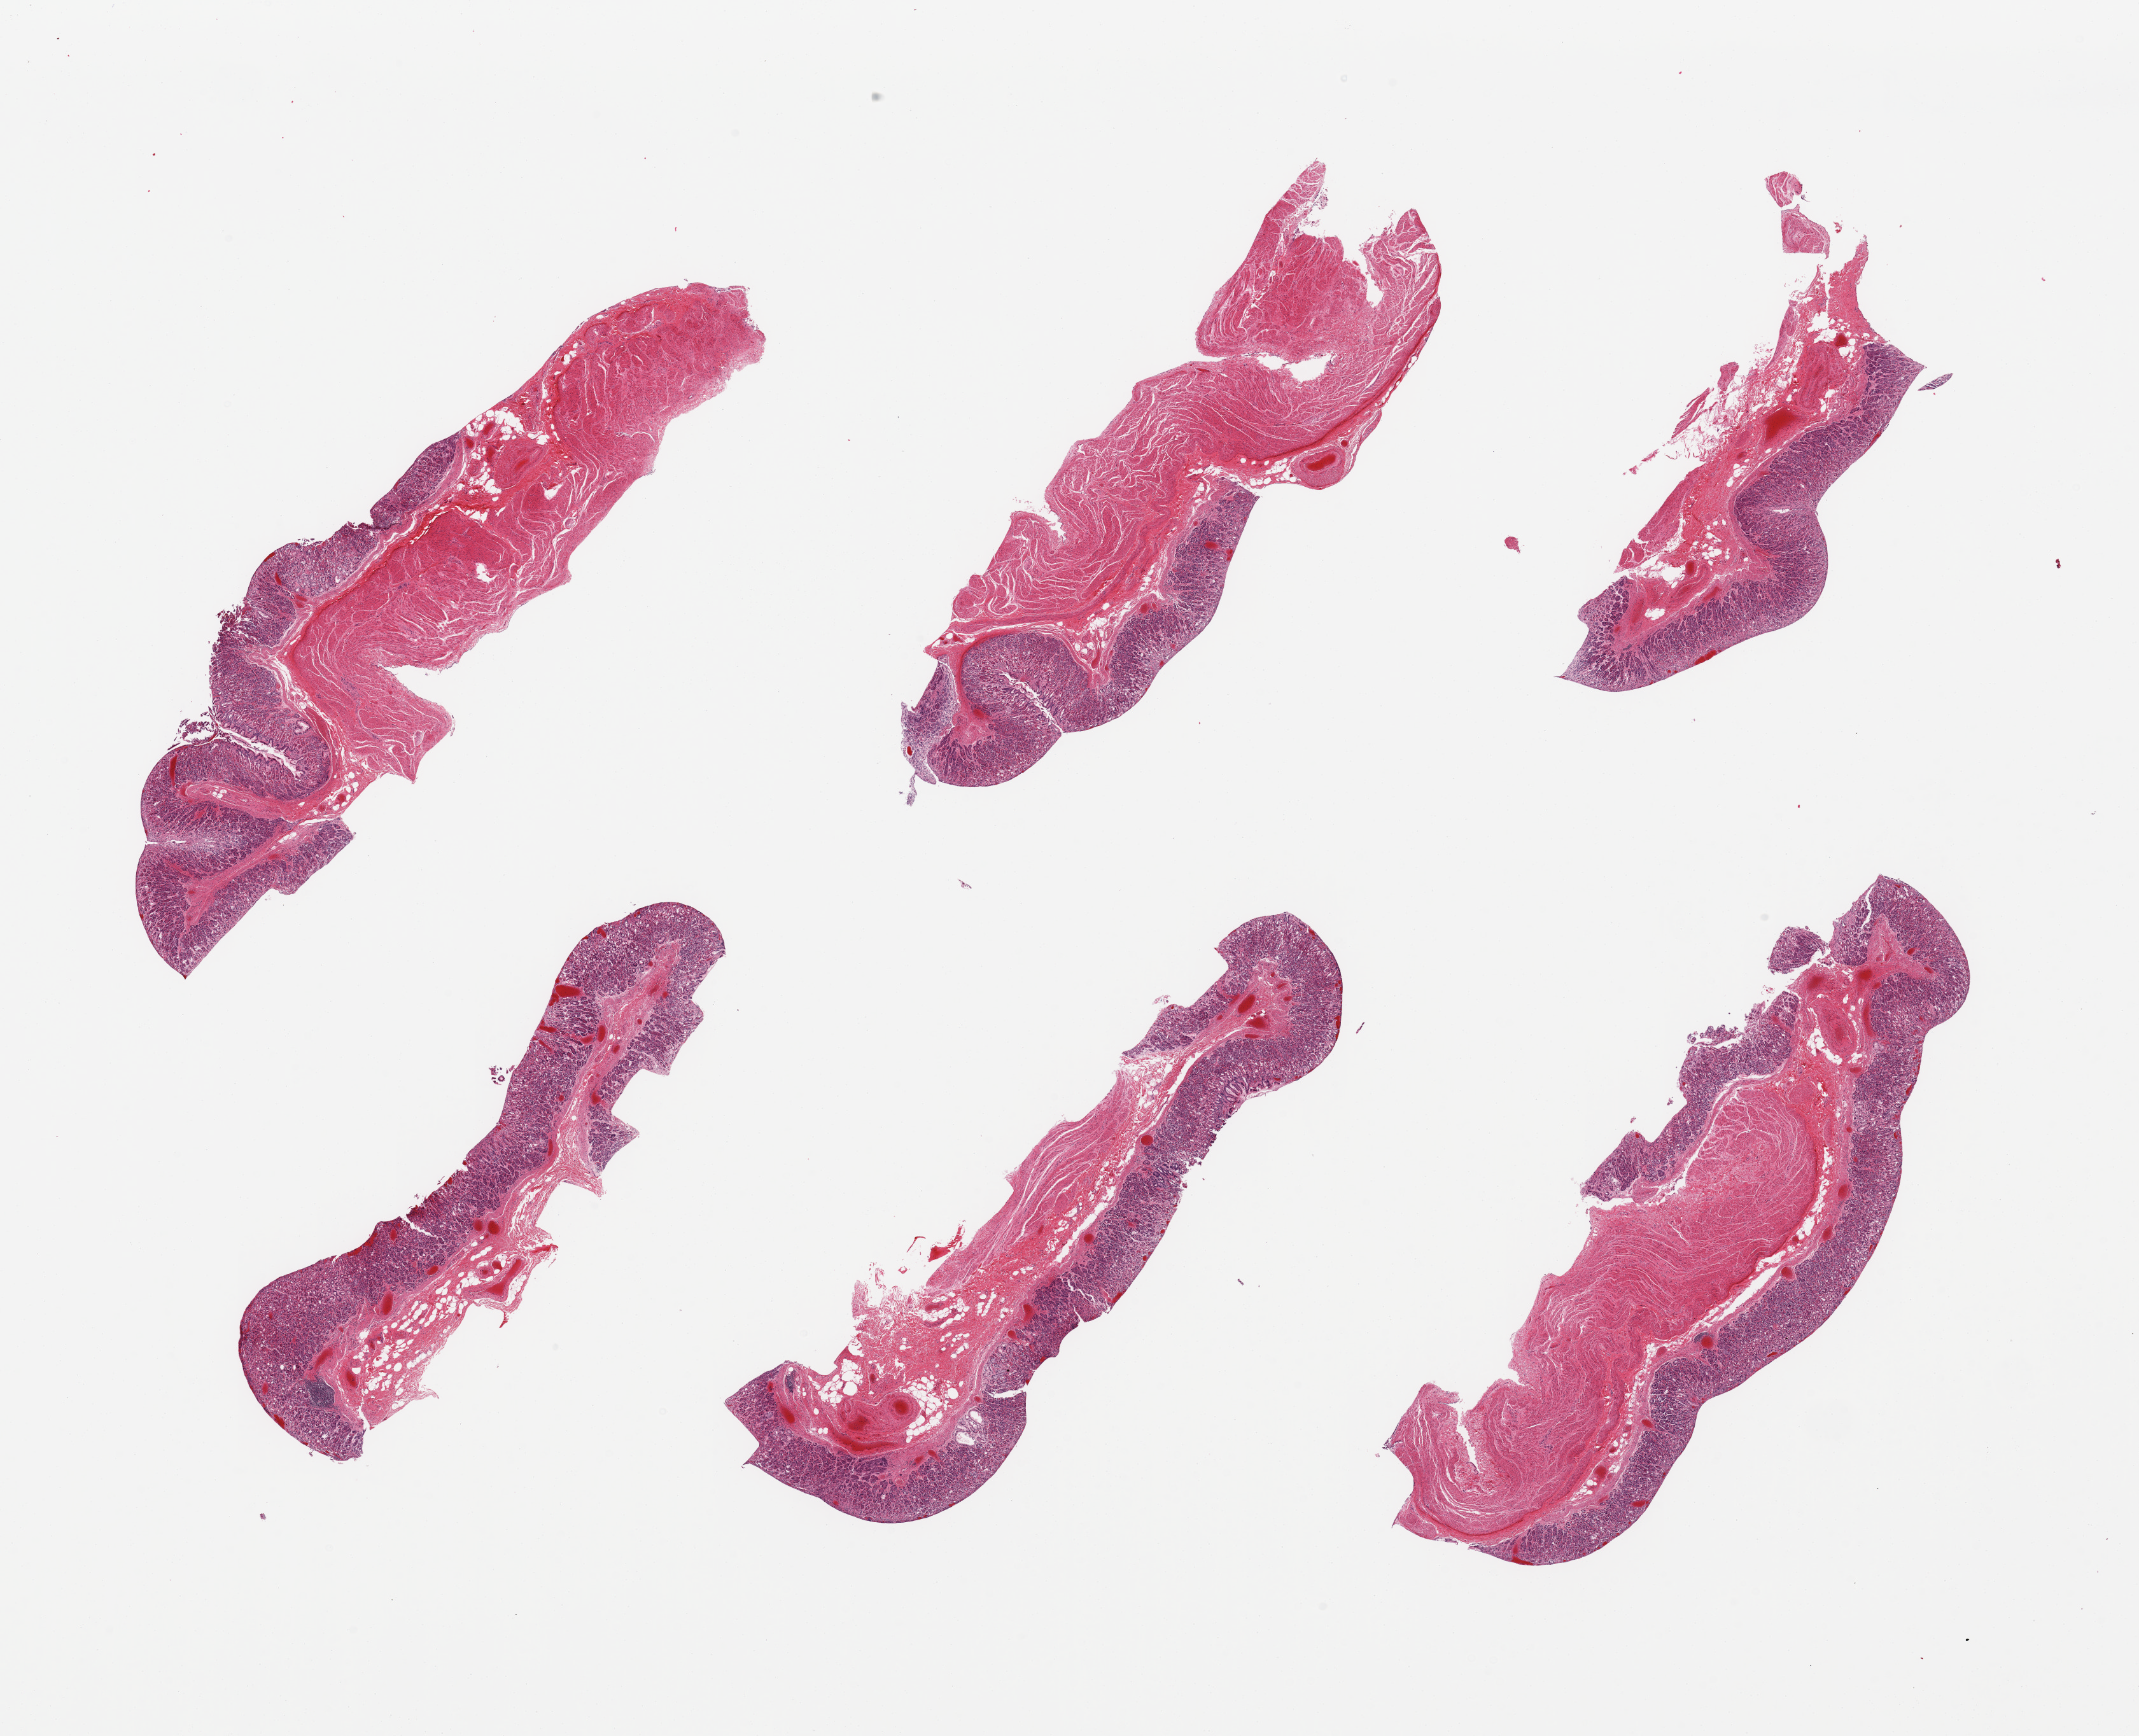
Whole-slide image, haematoxylin and eosin stain, low-resolution overview of the scanned area, about 26.6 x 21.6 mm (acquisition: 20x scan). PAXgene-fixed paraffin-embedded (PFPE) section. Target tissue: stomach. Tissue donor sample. Donor sex: male.
Reviewer comment on this tissue sample: 6 pieces; 2 pieces have little or no muscularis propria.